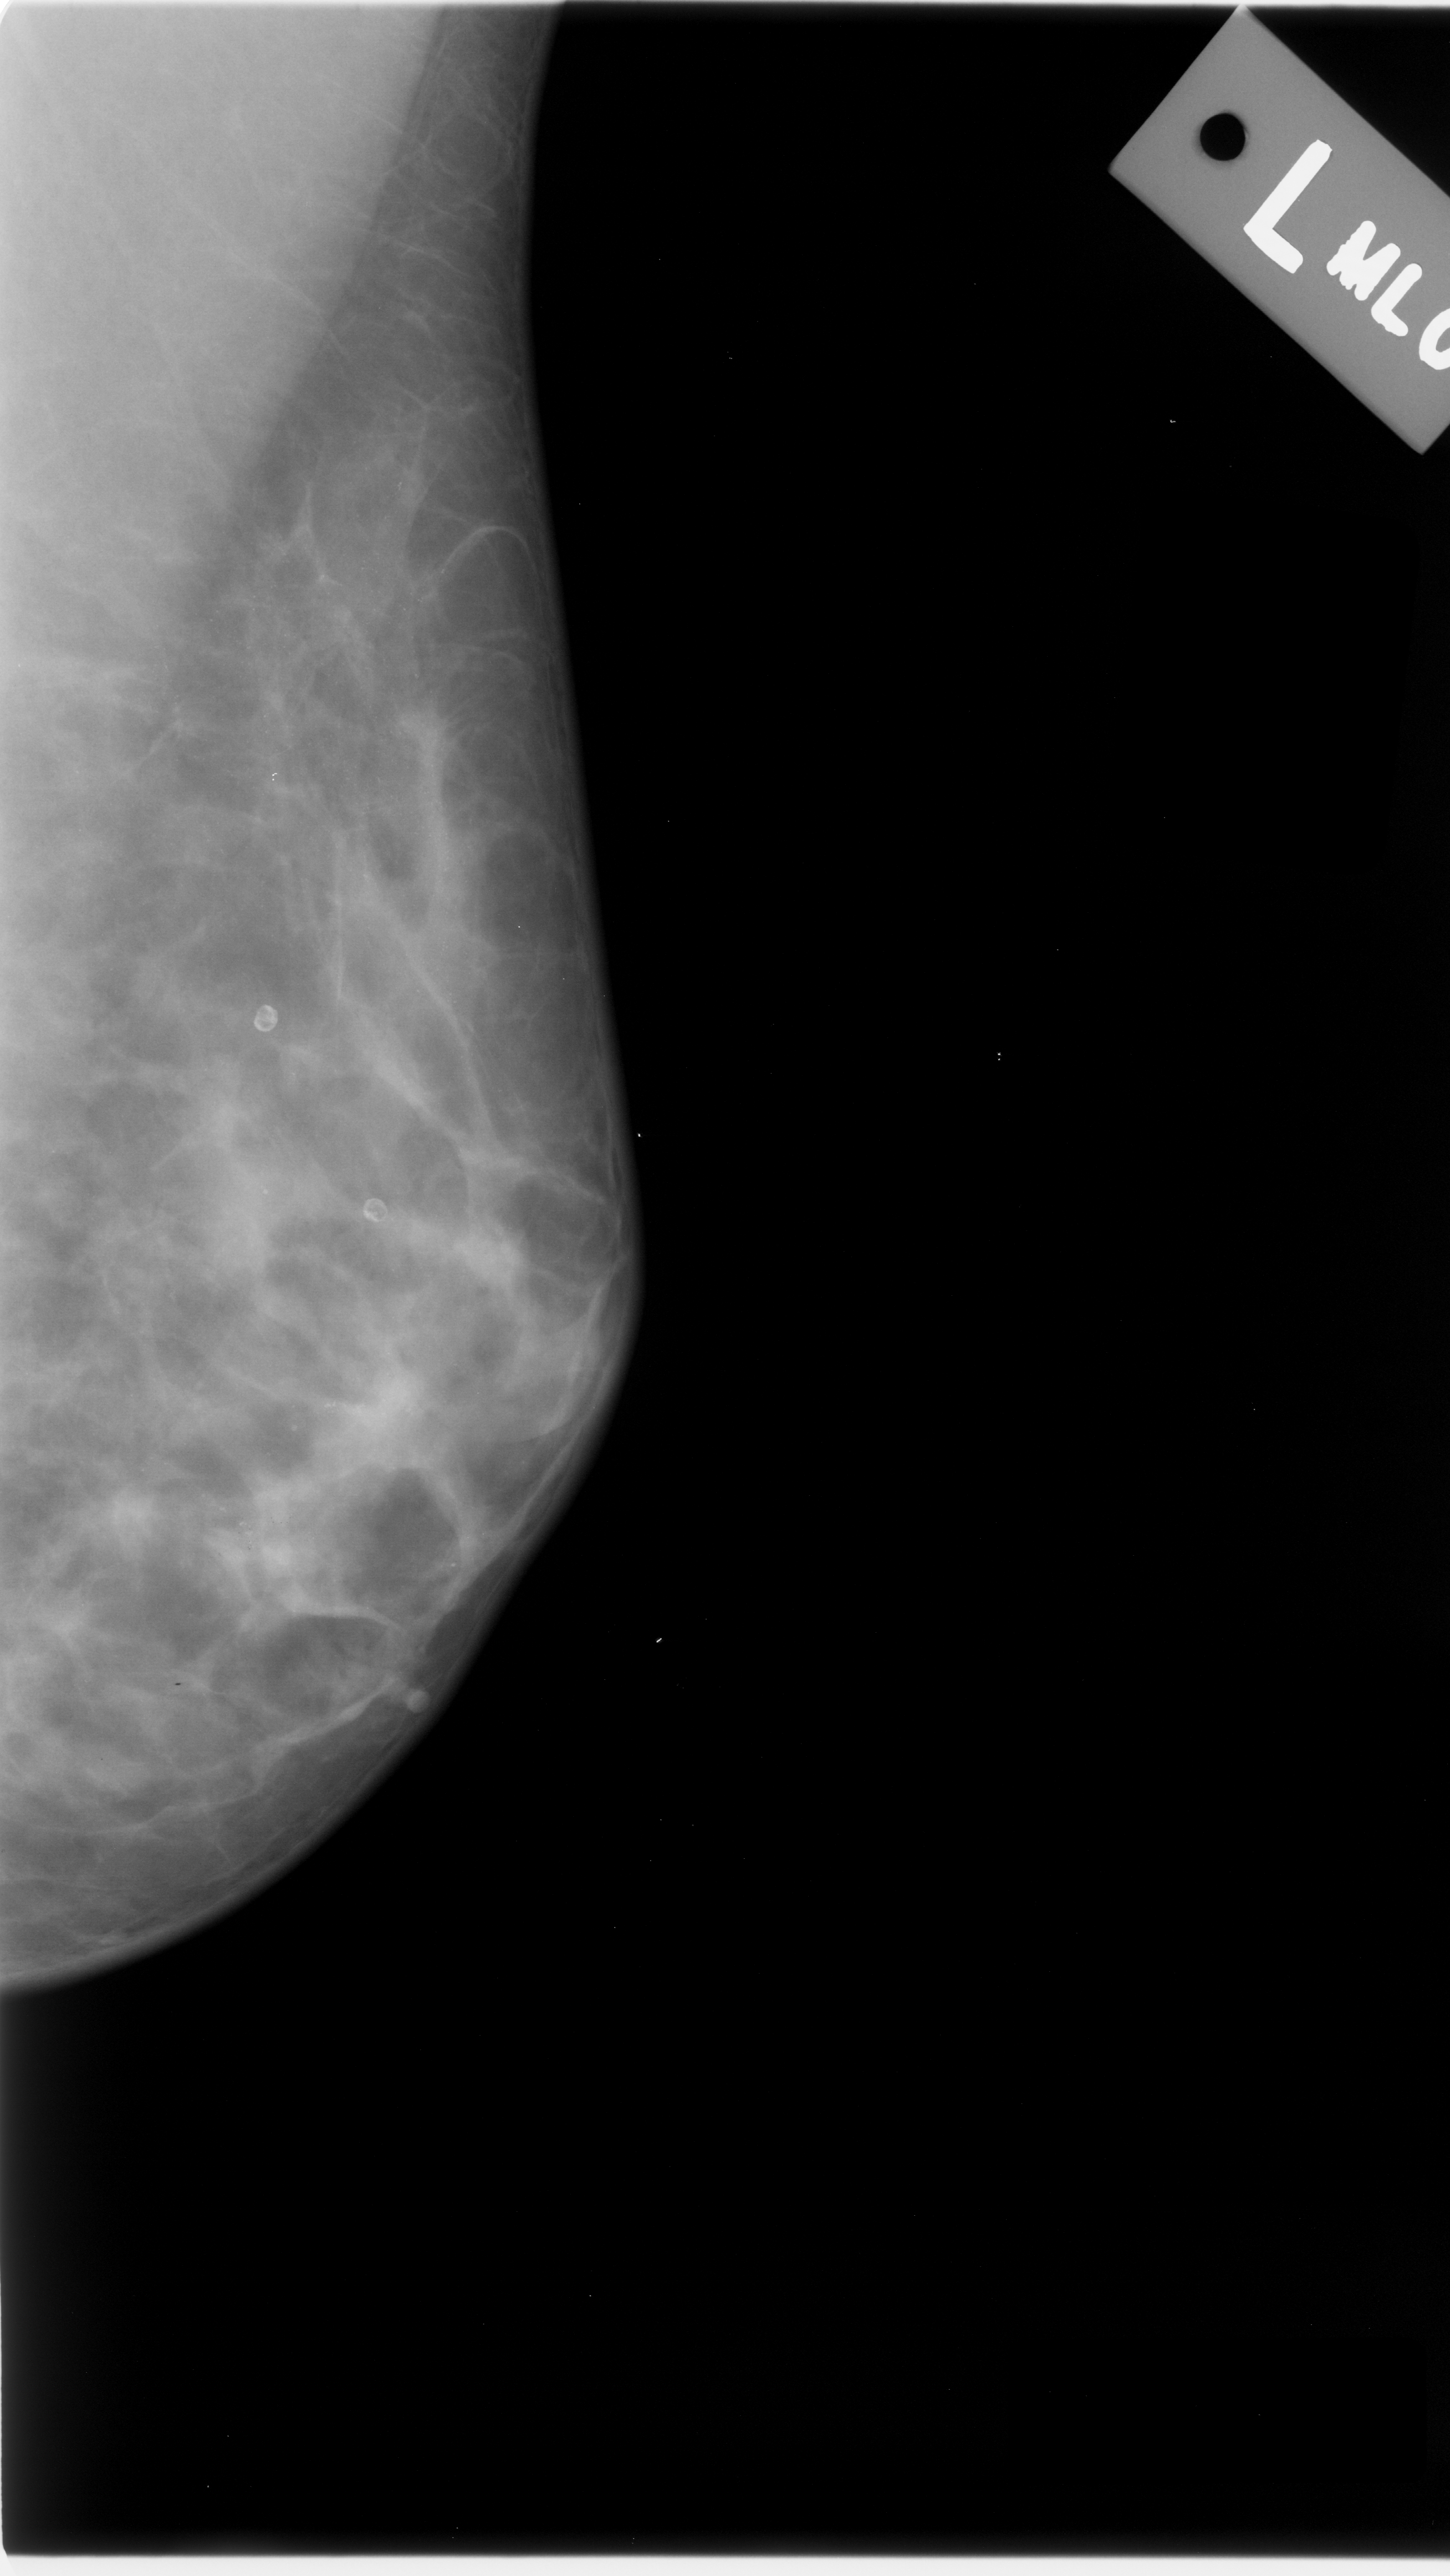
Scanned film-screen mammogram; left breast; mediolateral oblique (MLO) view.
Finding: calcifications, morphology amorphous, distribution diffusely scattered; BI-RADS assessment category 3; subtlety rating 4 on a 1 (subtle) to 5 (obvious) scale; pathology (as recorded): malignant.